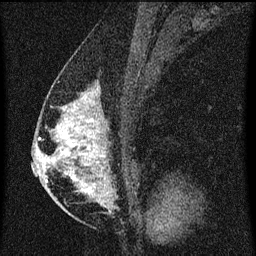
Breast MRI (dynamic contrast-enhanced), one sagittal slice. Position 32 of 60 along the scan axis. Dynamic contrast-enhanced series, image 2 of 3 at this slice position (ordered by acquisition). 1.5 T. TE 4.2 ms, TR 8 ms. 256 × 256 image matrix, field of view 180 × 180 mm. Patient: female, 47 years.
Outlined on this slice (semi-automatic segmentation, software-assisted and operator-edited):
- analysis volume of interest (the breast-tissue region the enhancement analysis was run in; not a lesion): bounding box <50,82,132,203> (left, top, right, bottom; pixels)
- tumour enhancement mask (voxels above the 70 % enhancement threshold inside the analysis volume of interest): <50,88,110,195>